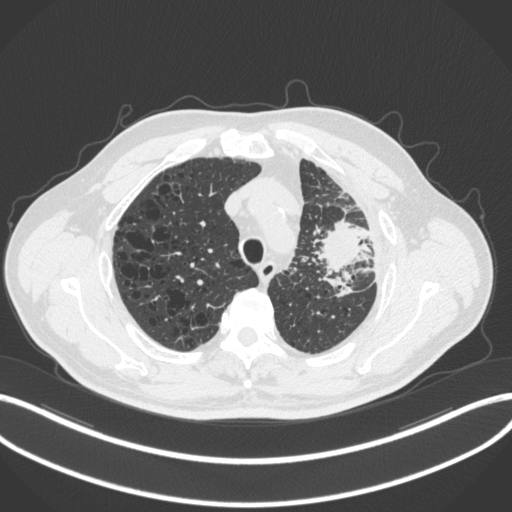
Chest CT, one axial slice. Slice 240 of 286 in the series (ordered by position). 120 kVp. Lung window (W 1500 / L -600 HU). 512 × 512 image matrix. Male patient, age 68 years. Case-level facts recorded for this patient, not image findings: clinical TNM (as recorded): T3 N3 M1.
Structures marked on this image (bounding box drawn by a radiologist):
- lung tumour (recorded histology: adenocarcinoma): bounding box [x1, y1, x2, y2] px = [318, 213, 366, 278]